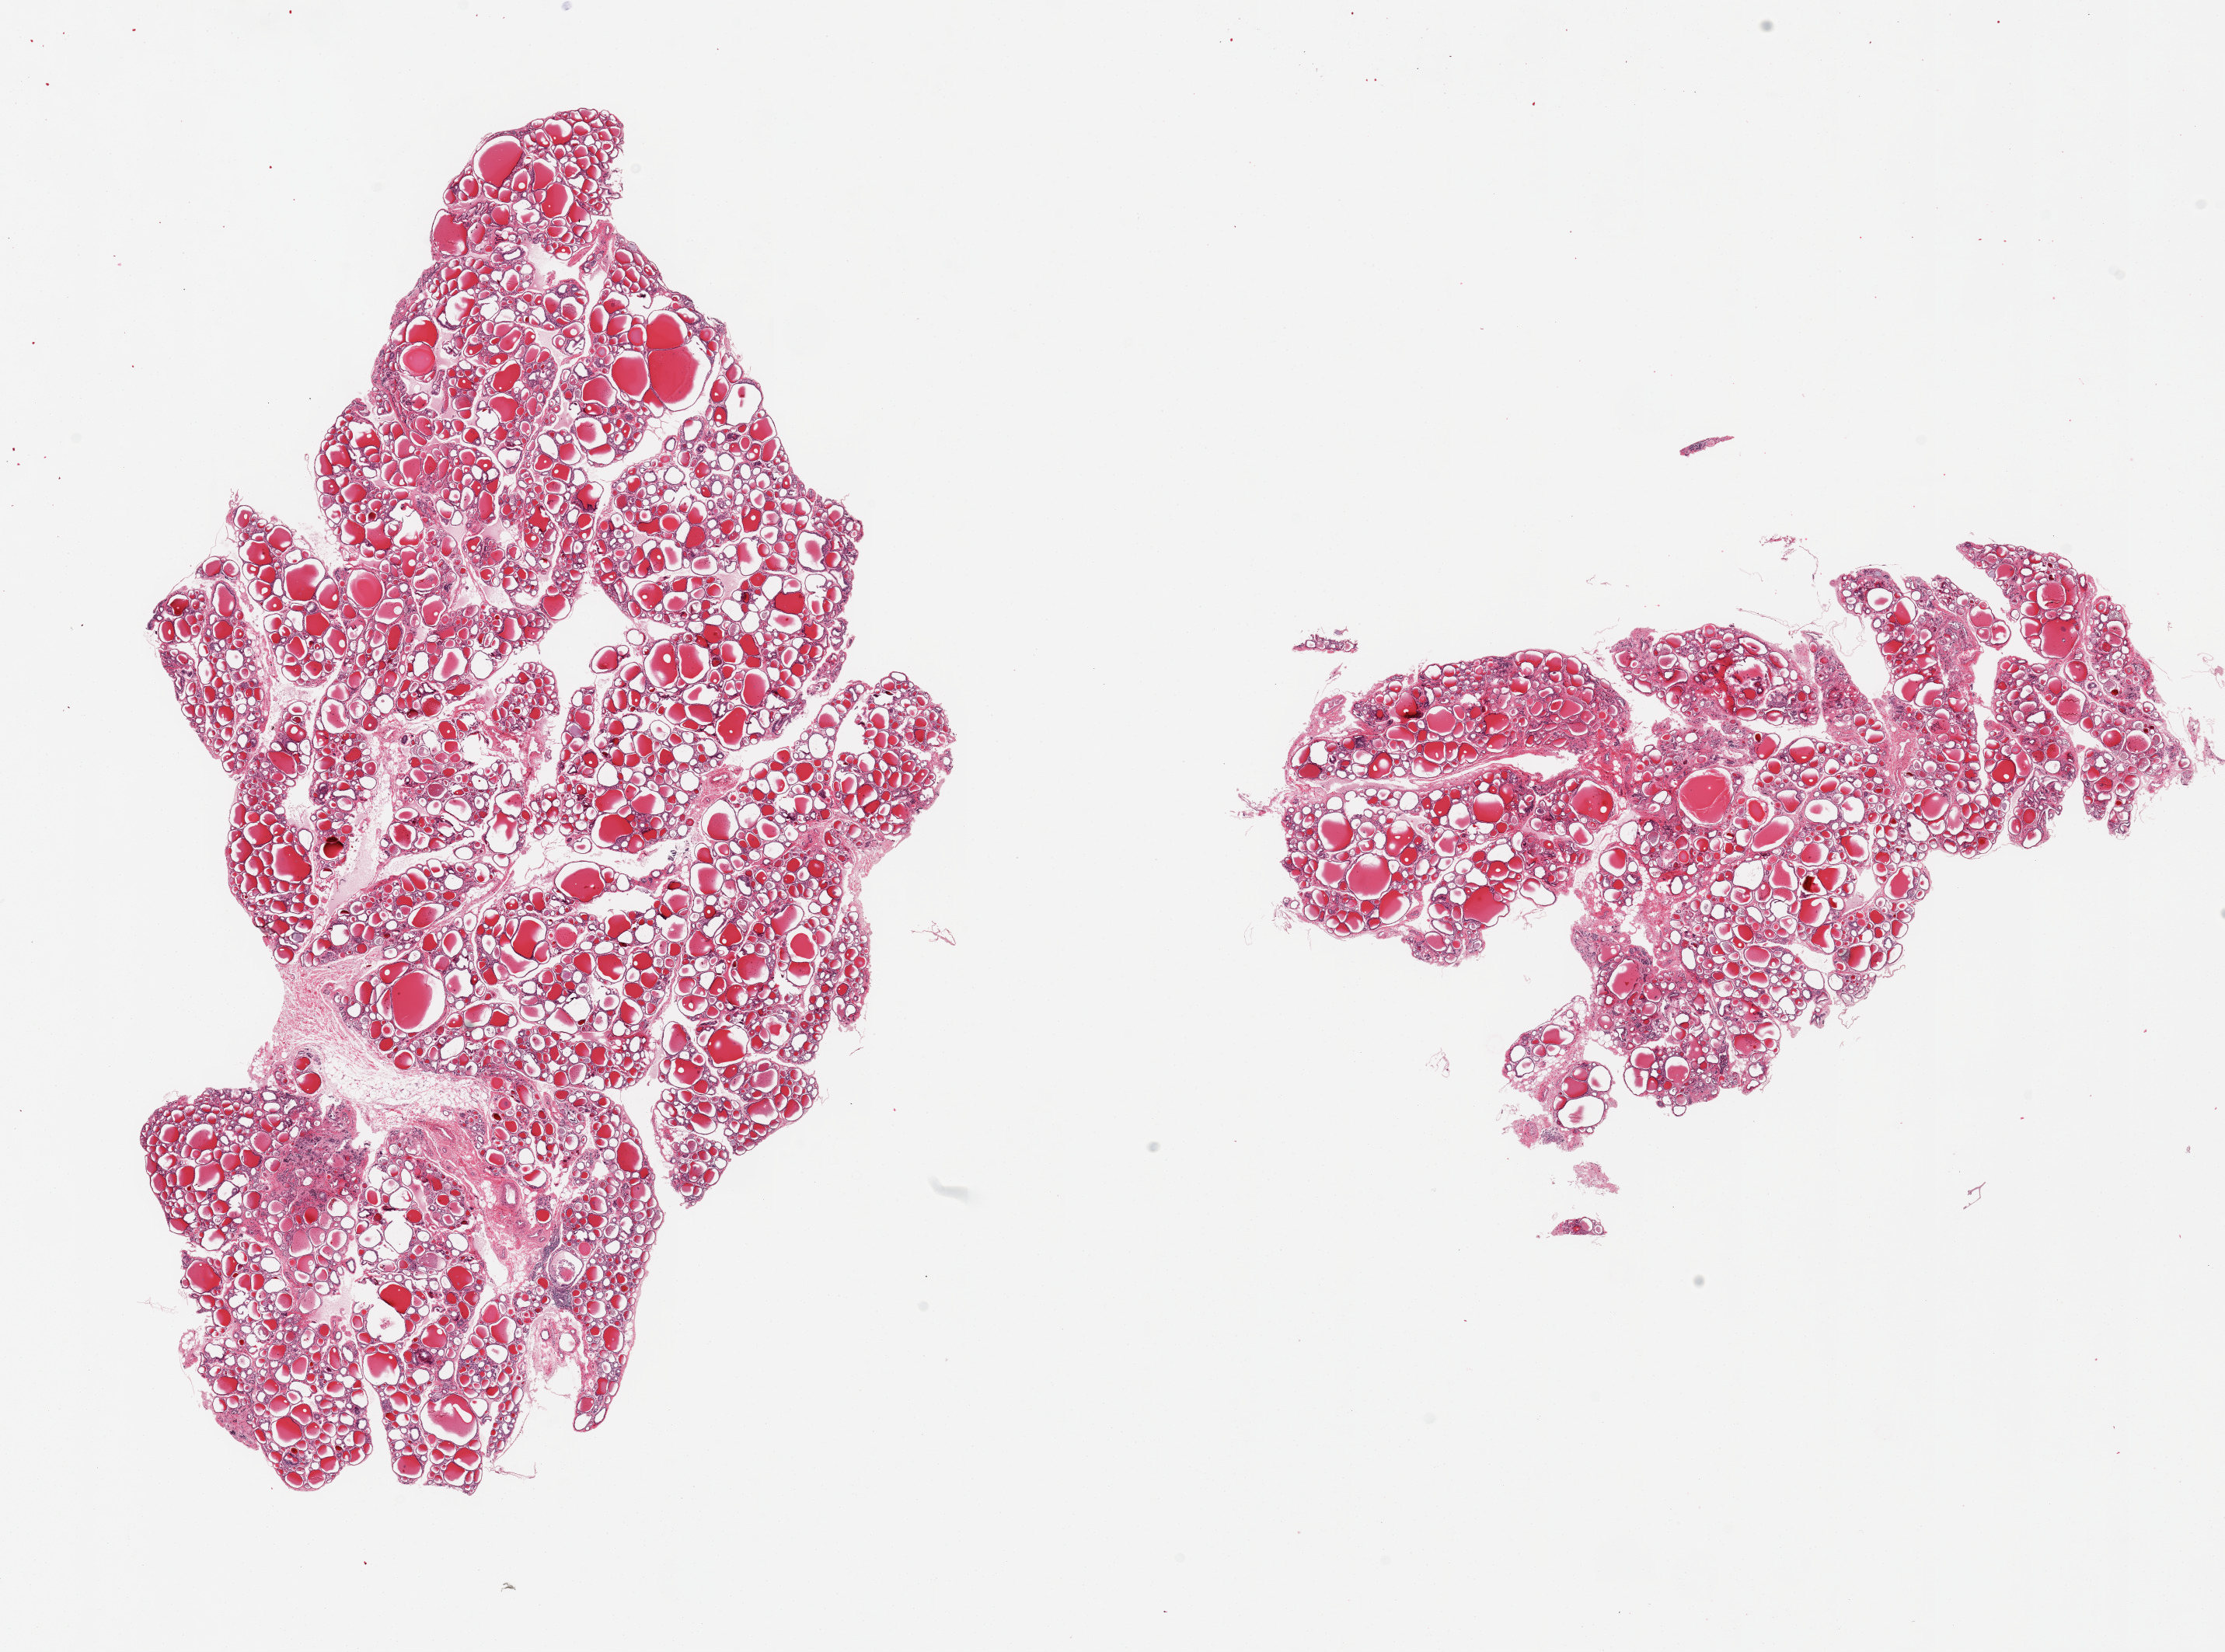
Digitized hematoxylin and eosin (H&E)-stained section, brightfield — whole scanned area (about 22.6 x 16.8 mm, from a 20x scan) shown as a low-resolution overview. PAXgene-fixed, paraffin-embedded tissue. Section of thyroid (target tissue). Tissue donor sample. Male donor.
Reviewer comment on this tissue sample: 2 pieces, no abnormalities.